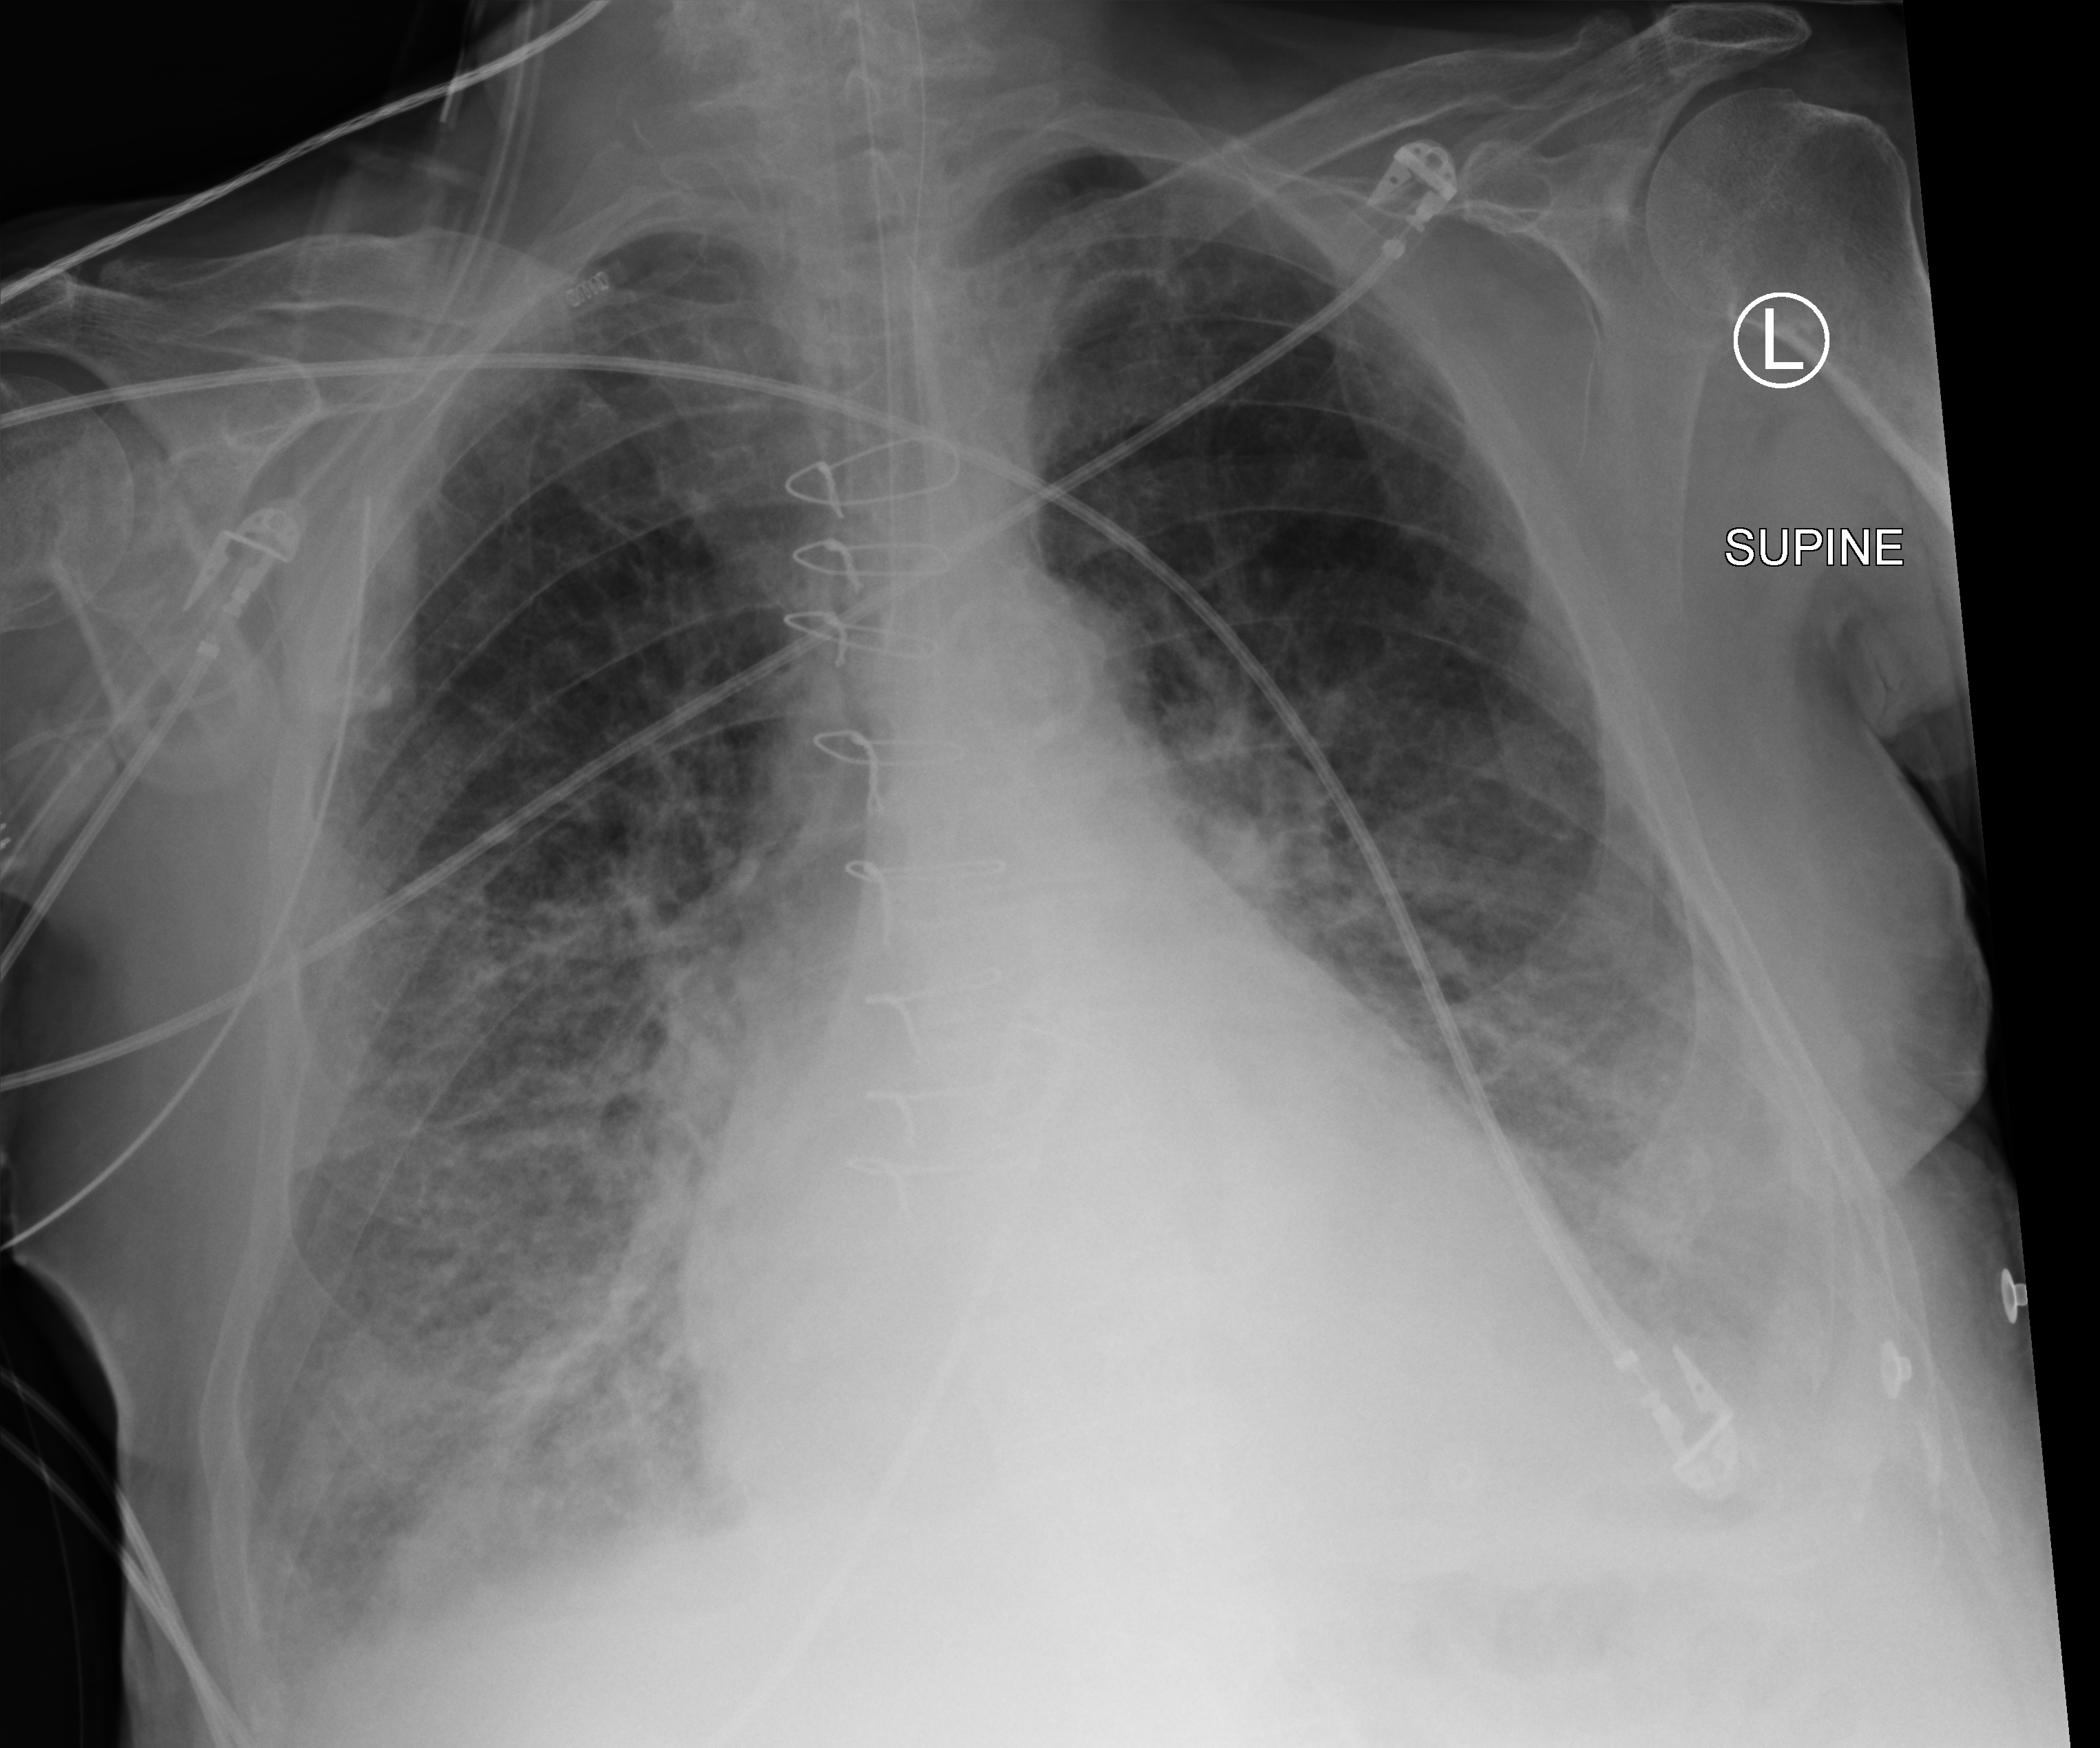
Bedside chest radiograph (computed radiography); anteroposterior (AP) projection. Male patient hospitalised with COVID-19, age 75–90 years.
Hospital-stay facts (about this admission, not read from this image; timing relative to this image not recorded): mechanically ventilated during this hospital stay: yes.